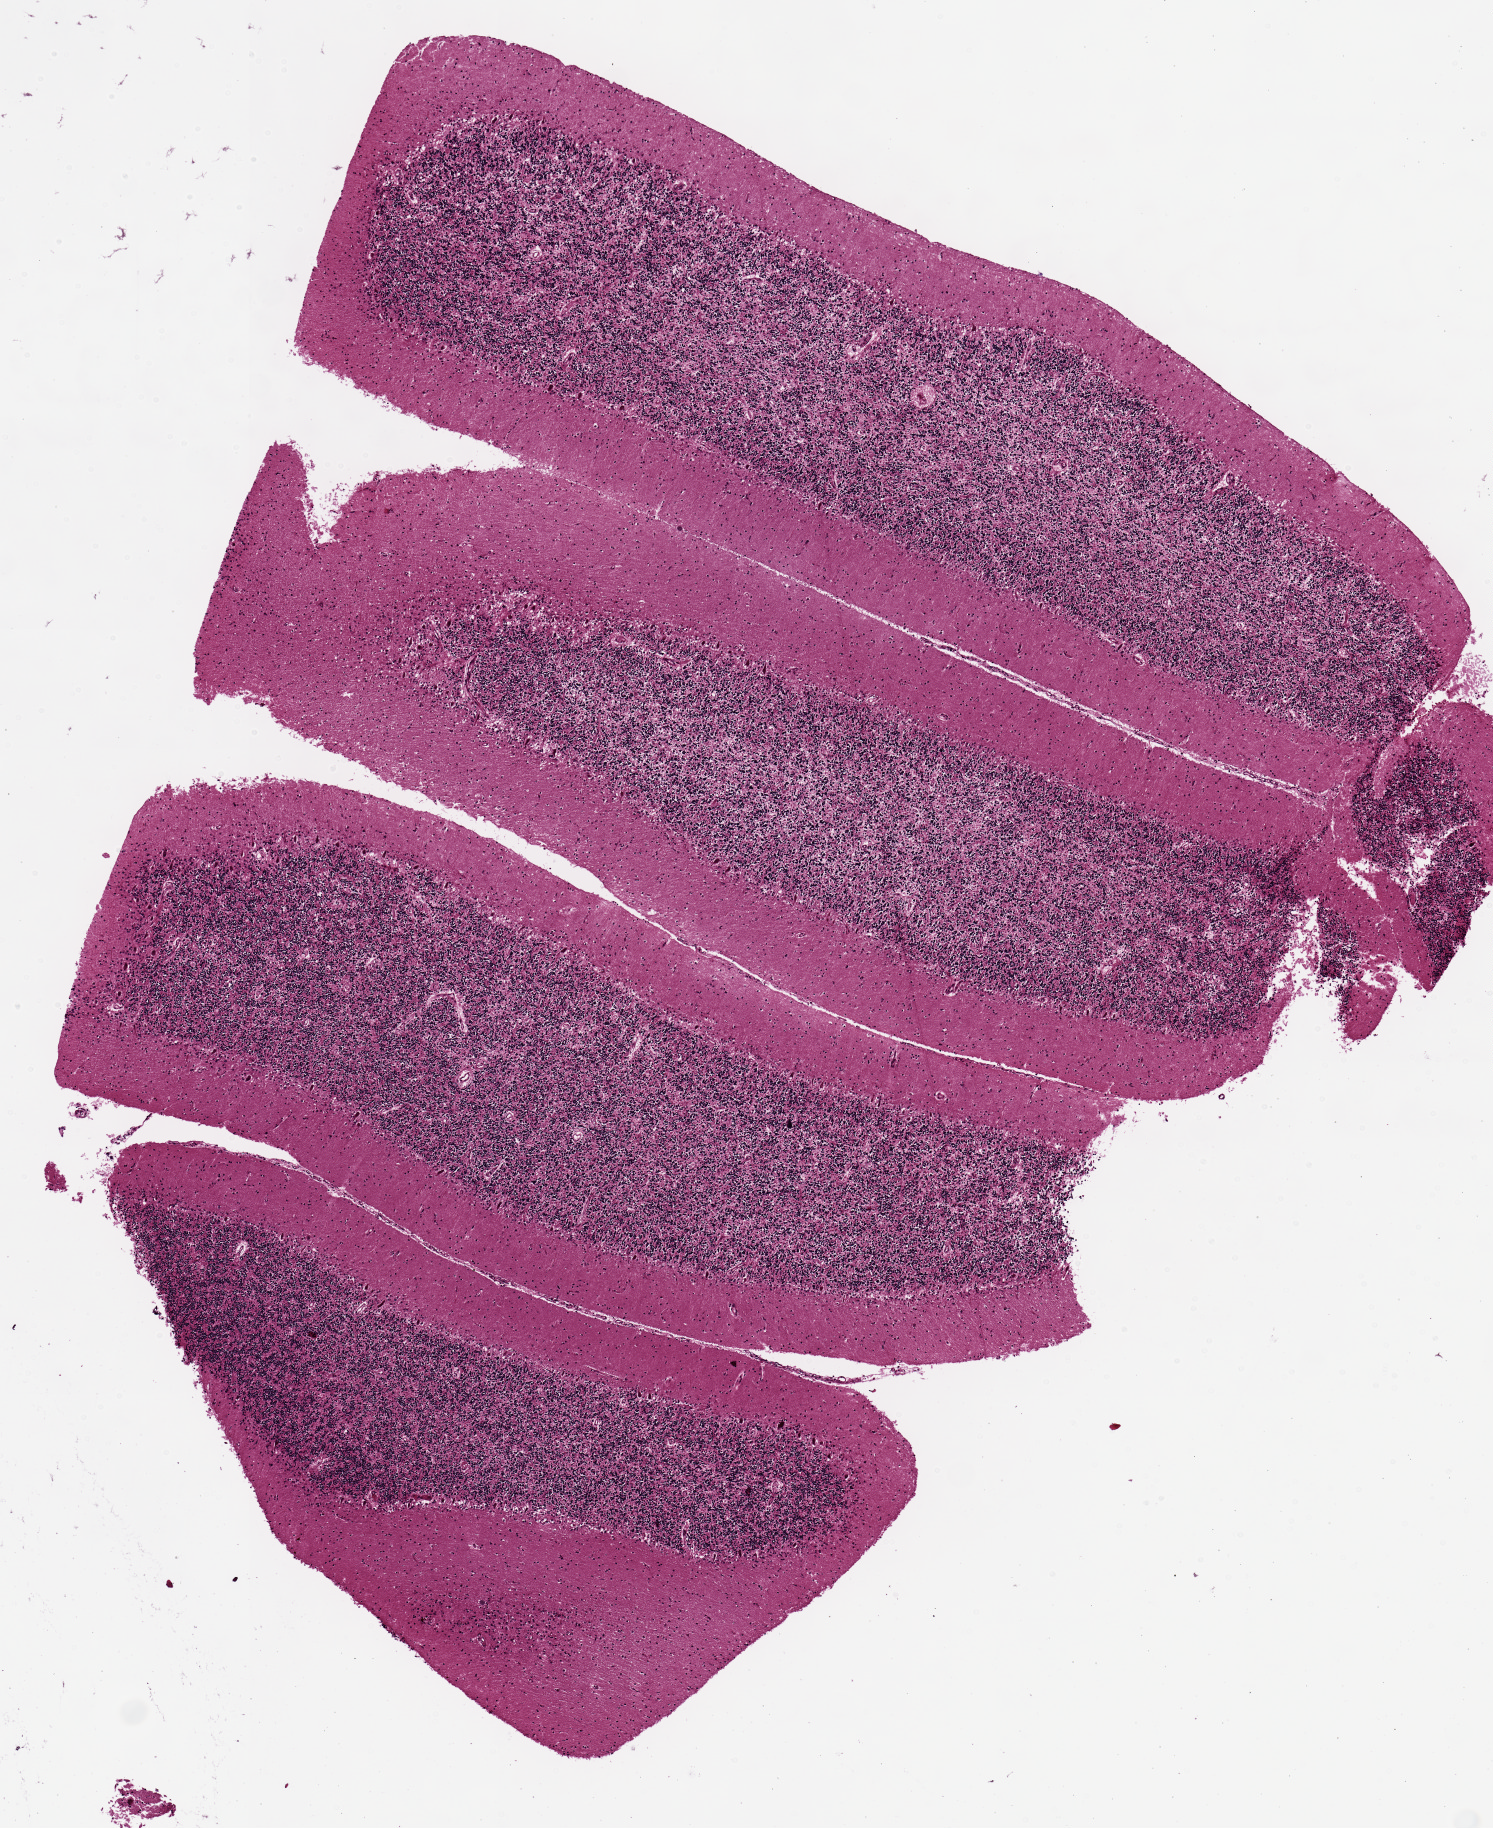
Whole-slide image, hematoxylin and eosin (H&E) stain, brightfield — low-resolution overview of the scanned area, about 5.9 x 7.2 mm; PAXgene-fixed paraffin-embedded (PFPE) section; section of cerebellum (target tissue); tissue donor sample. Donor sex: female.
* reviewer comment on this tissue sample: 2(granular layer) 1 (cortex)